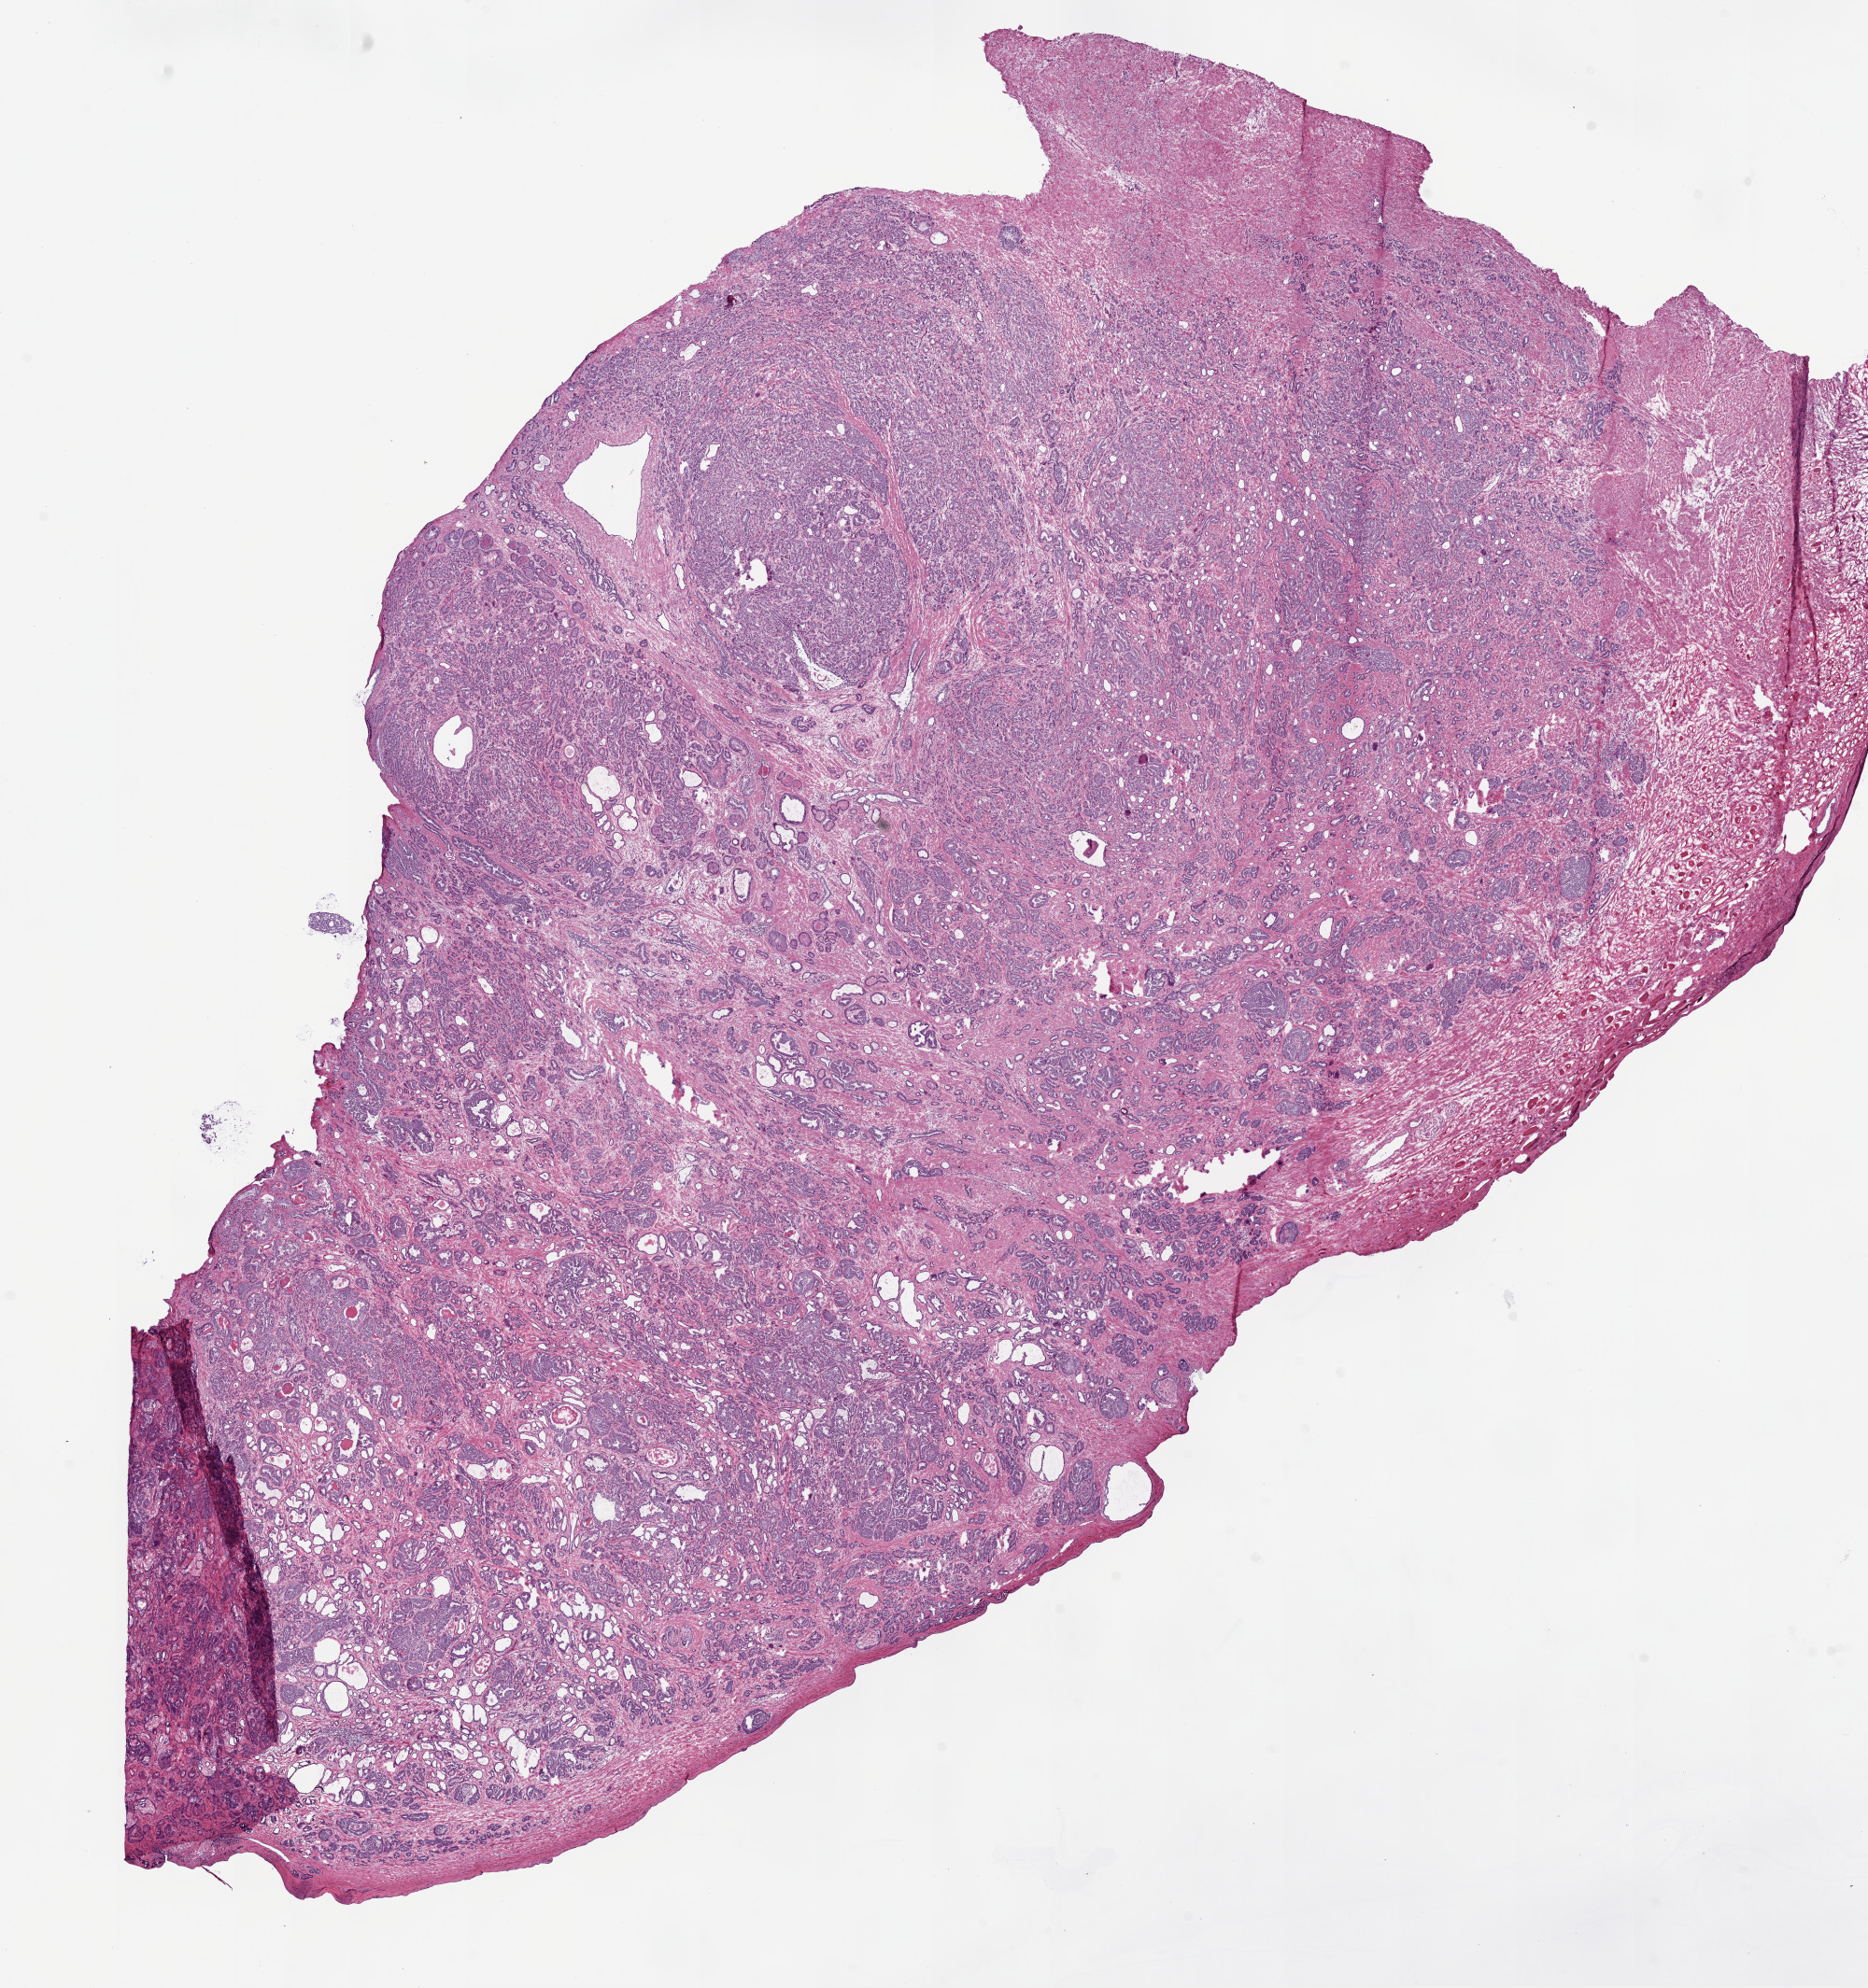
Digitized H&E tissue section (whole slide), a low-resolution overview of the entire scanned area, about 16.0 x 17.1 mm (from a 20x scan); frozen section from the top of the tissue portion; sample: primary tumour, prostate. Male patient; age at initial diagnosis 55 years. Gleason score: 7 (3+4). Slide review estimates, as recorded: tumour cells 70%, tumour nuclei 75%, normal cells 15%, stromal cells 15%, necrosis 0%. Inflammatory infiltration, as recorded: lymphocyte infiltration 1%, monocyte infiltration 0%, neutrophil infiltration 0%.
- histologic diagnosis: Acinar cell carcinoma (prostate gland)
- laterality: bilateral